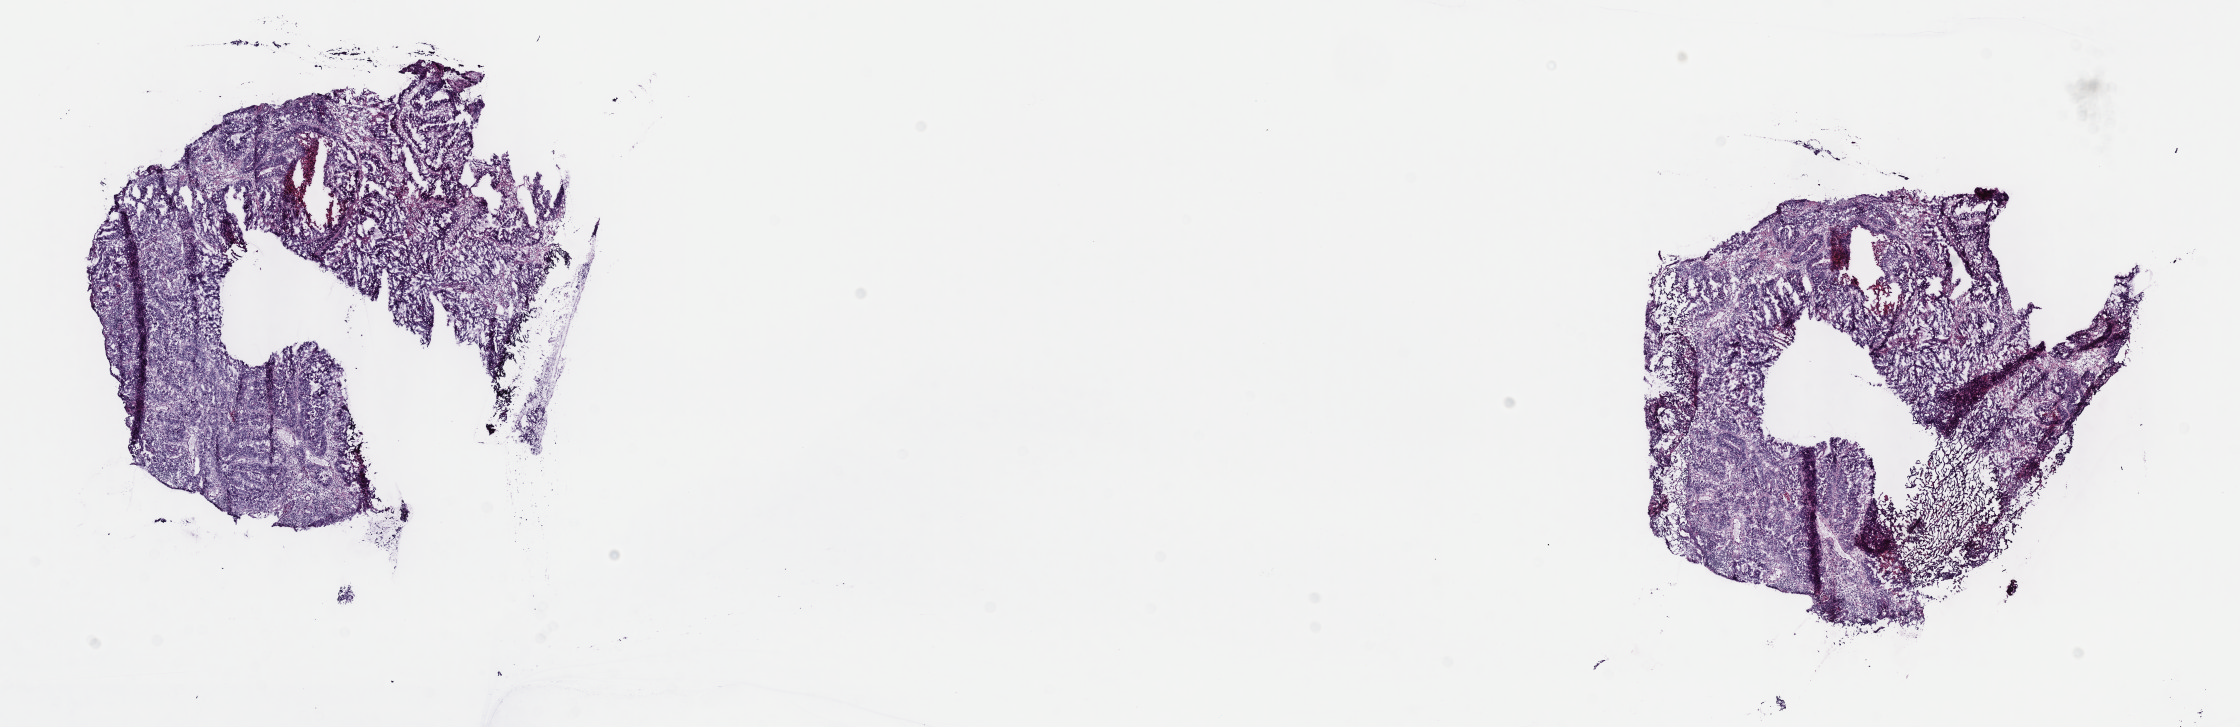
Digitized H&E-stained tissue section (whole slide) — whole scanned area (about 18.1 x 5.9 mm, acquisition: 40x scan) shown as a low-resolution overview; frozen section; primary tumour sample from the colon. Male, age 76 years at initial diagnosis. Pathologist review of this section (percent, as recorded): tumour cells 80%, tumour nuclei 80%, normal cells 8%, stromal cells 8%, necrosis 4%. Infiltration values recorded for this section: lymphocyte infiltration 5%, monocyte infiltration 0%, neutrophil infiltration 2%.
Diagnosis: Adenocarcinoma, NOS (ascending colon). AJCC pathologic stage: IIA. Lymph nodes positive (case pathology): 0 of 15 examined.